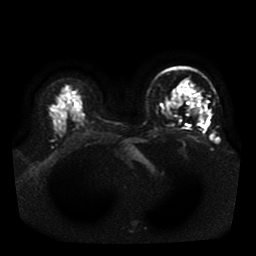
Breast MRI, one axial slice. Position 29 of 41 along the scan axis. Diffusion-weighted series; image 2 of 4 stored at this slice position (different b-values; order by instance number). 1.5 T. 5 mm slice thickness. 256 × 256 image matrix, field of view 330 × 330 mm. Female patient.
Structures marked on this image (expert manual segmentation):
- tumour on diffusion-weighted imaging: bounding box (x1, y1, x2, y2) in pixels: (204, 112, 208, 122)